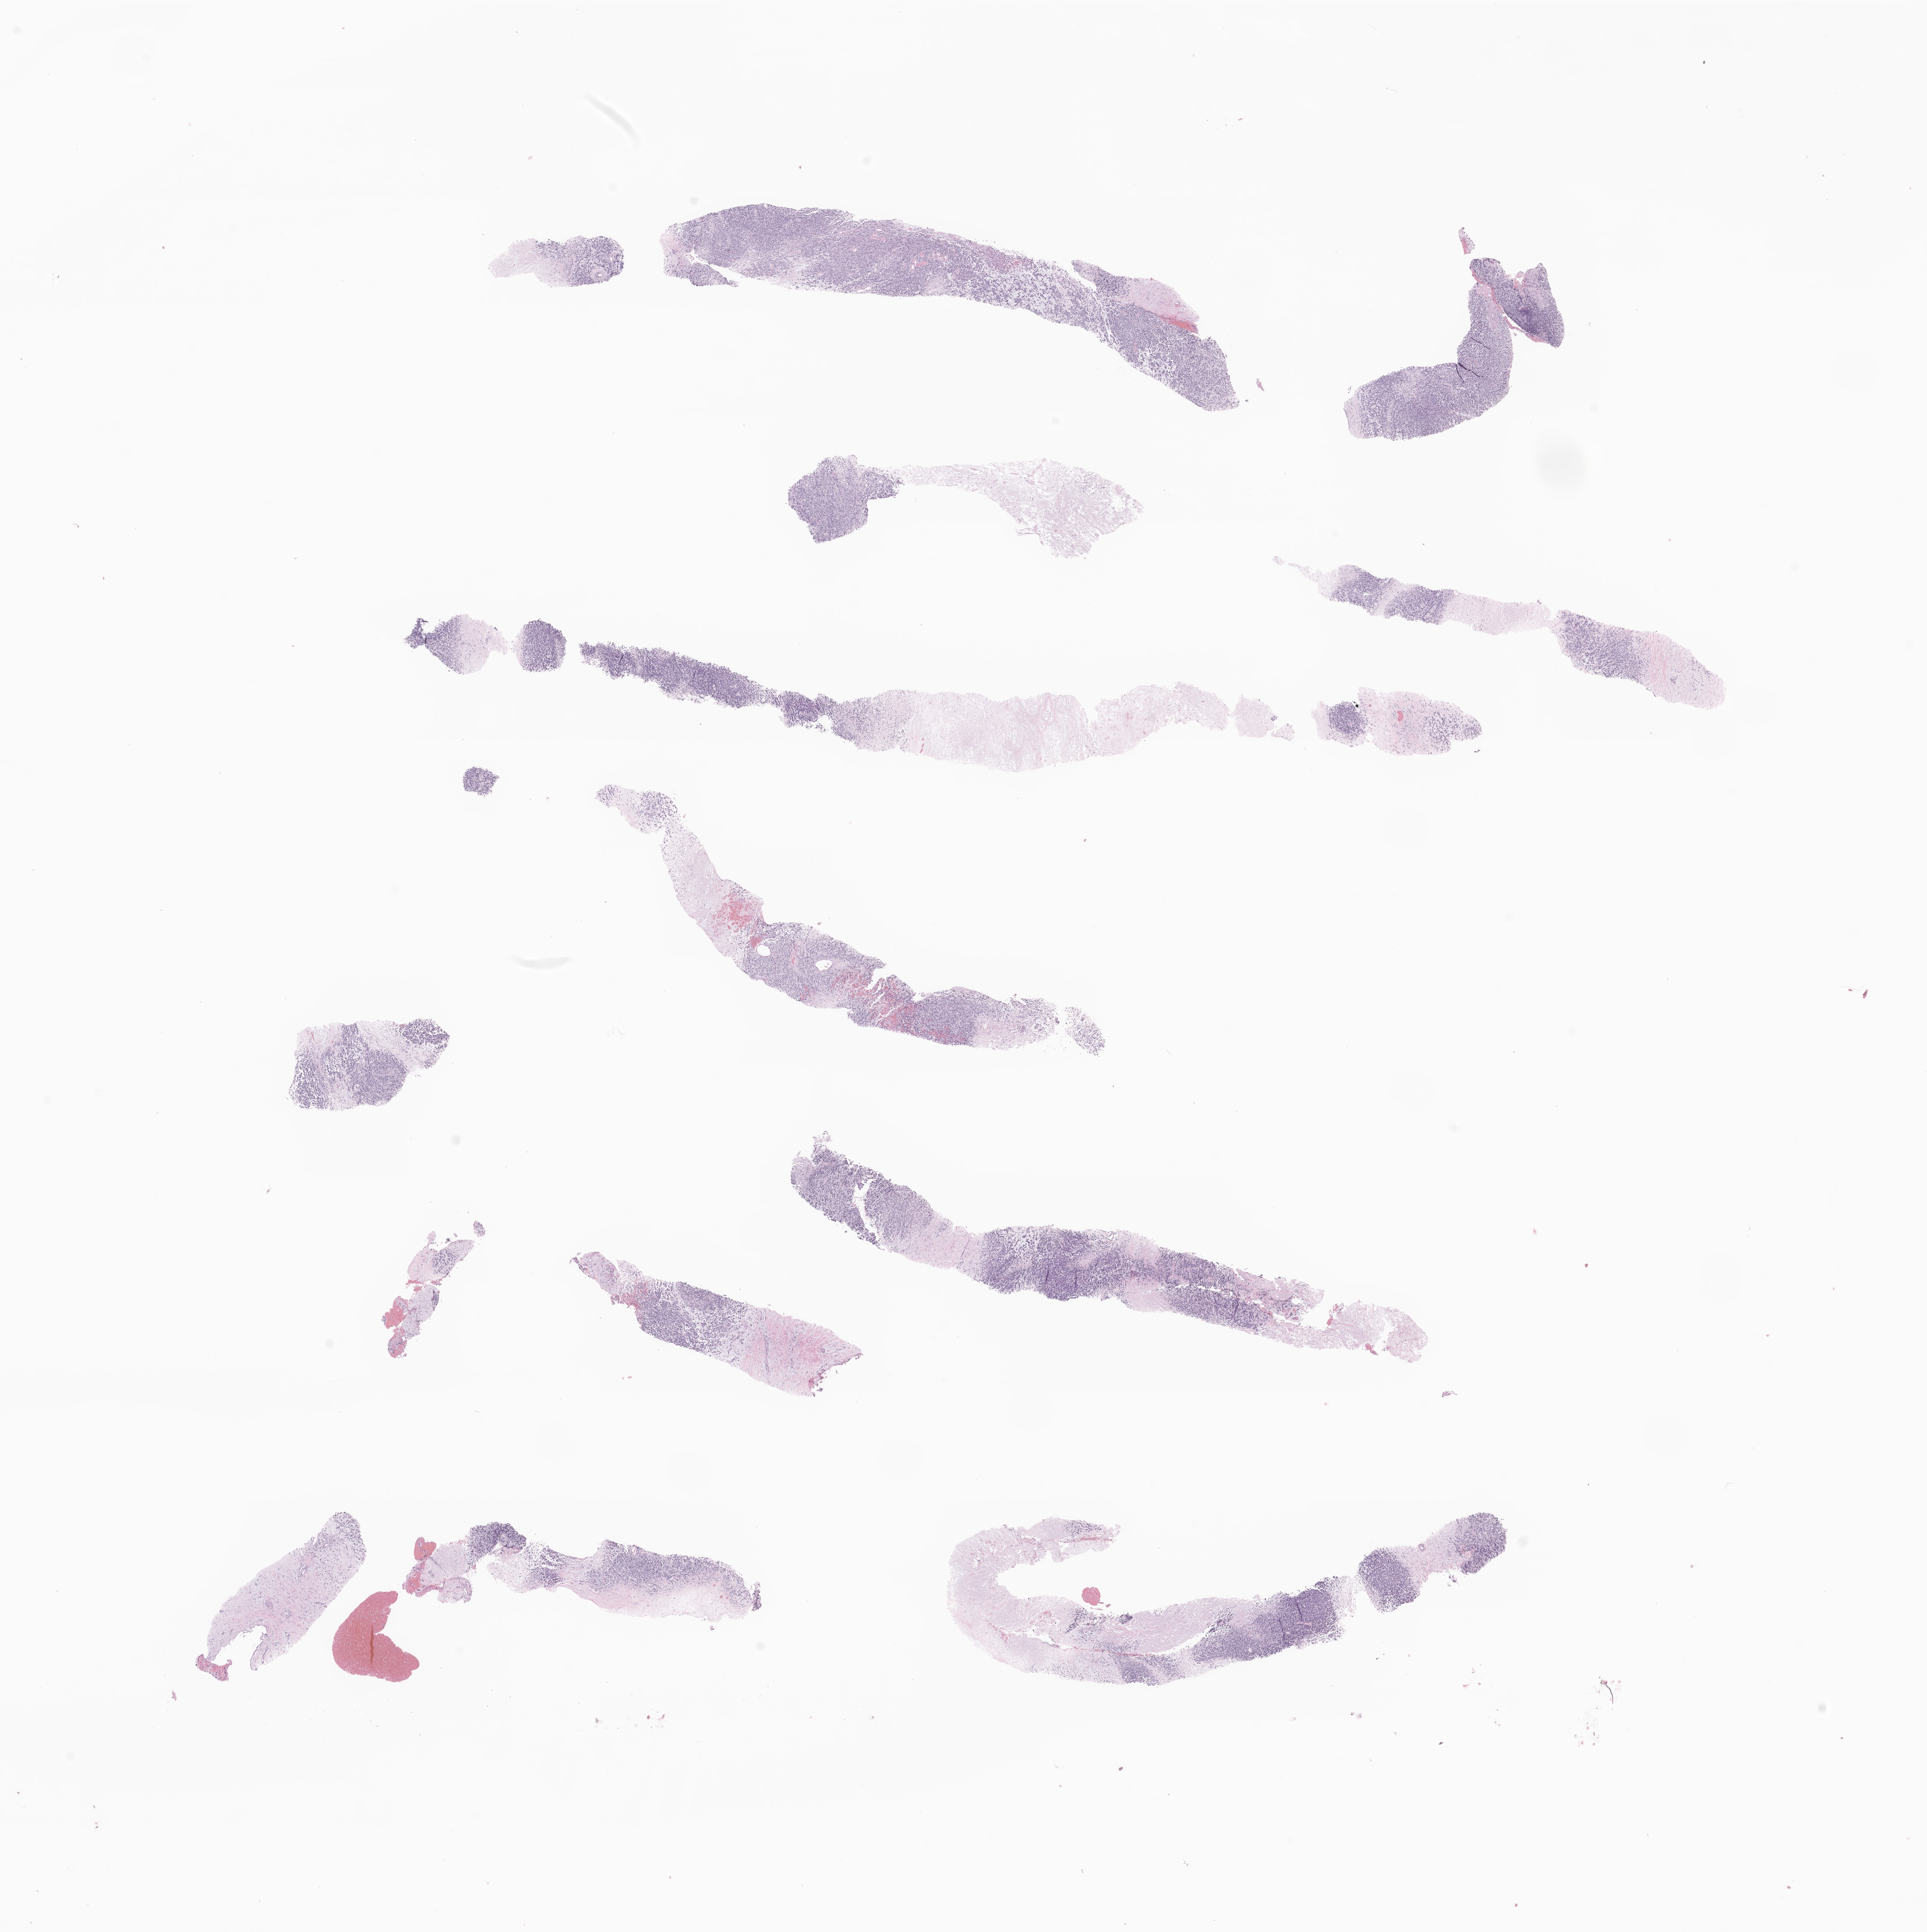
Digitized H&E-stained section of tumor tissue from the pelvis, shown as a low-resolution overview of the whole scanned area (about 18.9 x 19.0 mm). Formalin-fixed paraffin-embedded section. Male patient, age 220 months (18 years 4 months).
- diagnosis: Desmoplastic small round cell tumor